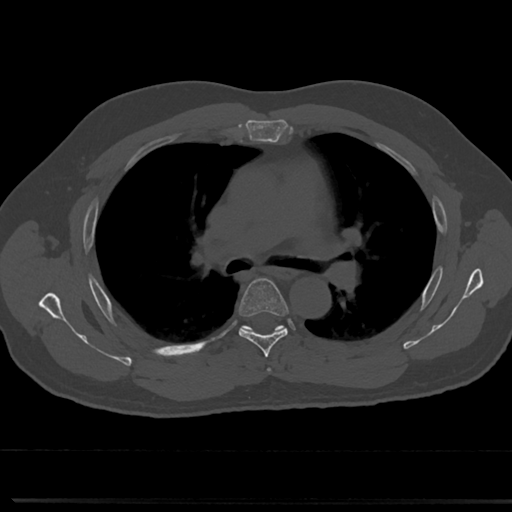
CT including the spine, one axial slice; position 491 of 817 along the scan axis; reconstruction kernel Br40s/3; 120 kVp; bone window (W 1800 / L 400 HU); 0.5 mm slice thickness; 512 × 512 image matrix, field of view 355 × 355 mm. Patient: male, 61 years. From the clinical record (not read from this slice): primary cancer: prostate.
Structures marked on this image (semi-automatic segmentation, software-assisted and operator-edited):
- T4 vertebra: bounding box [x1, y1, x2, y2] px = [264, 361, 273, 374]
- T5 vertebra: [219, 278, 300, 348]